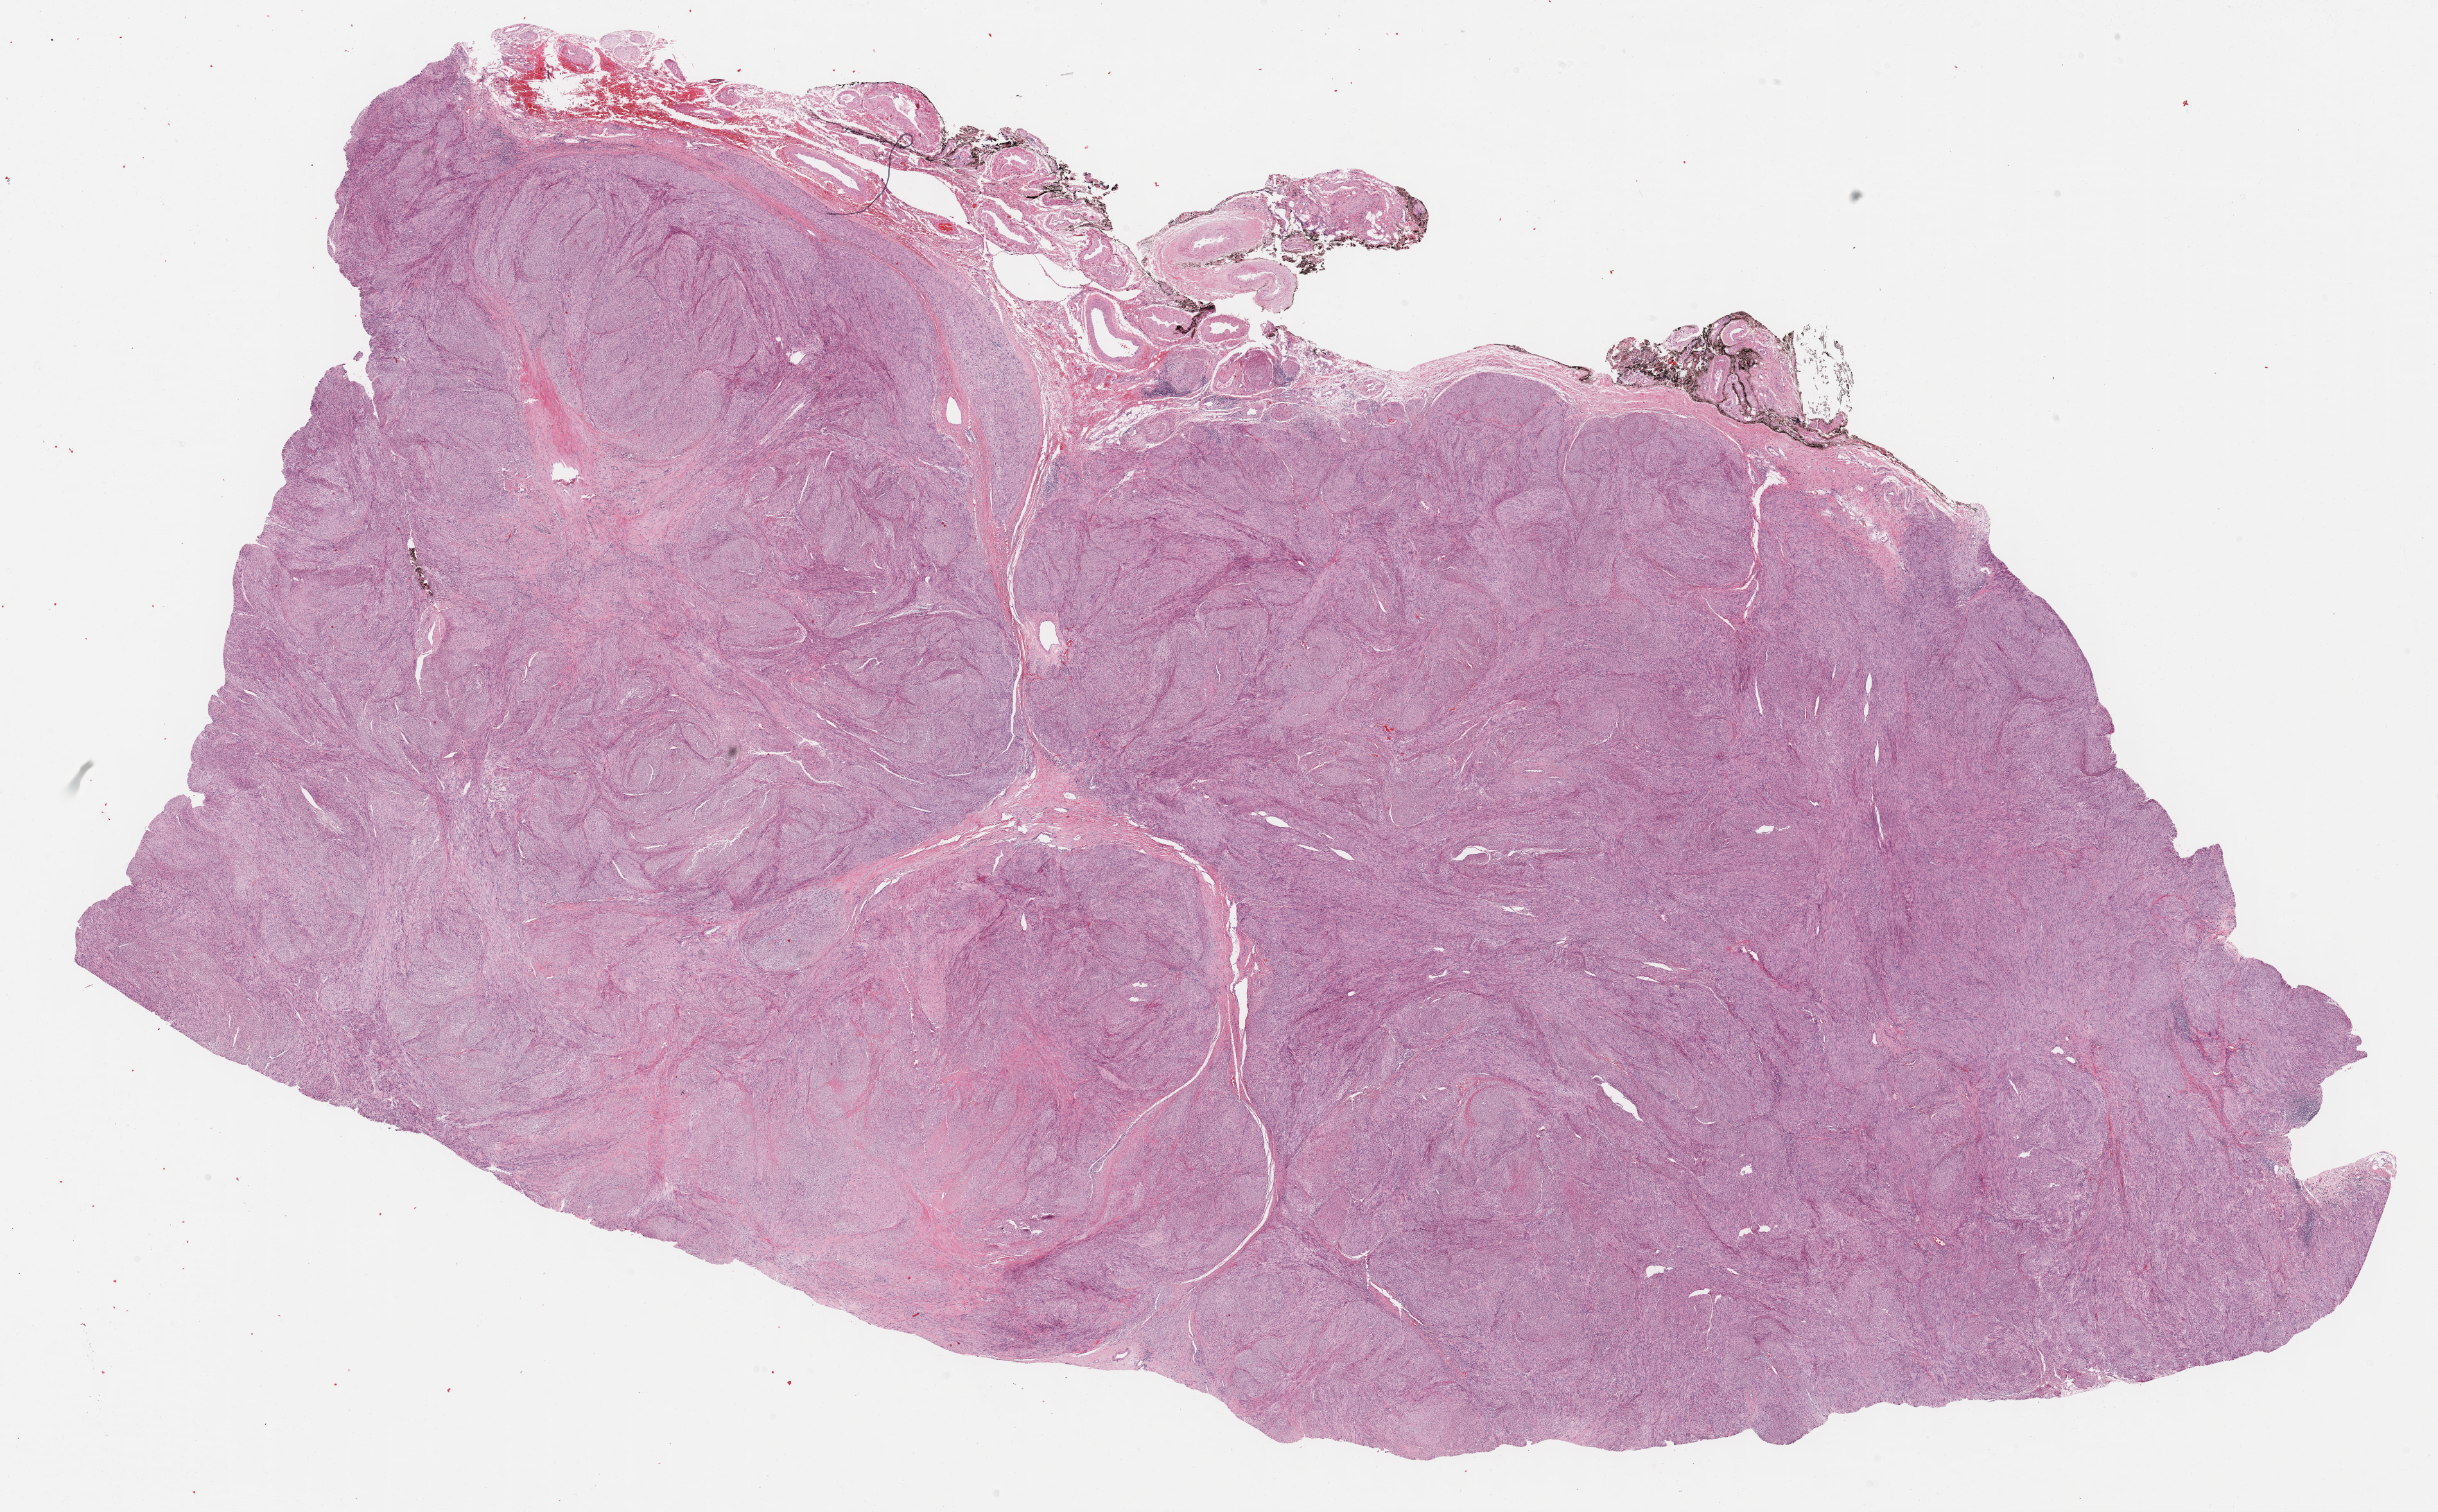
Whole-slide histology image, H&E — shown as a low-resolution overview of the whole scanned area (about 30.7 x 19.0 mm). Formalin-fixed paraffin-embedded (FFPE) diagnostic section. Sample: primary tumour, retroperitoneum and peritoneum. Female, age 78 years at initial diagnosis.
Histologic diagnosis: Dedifferentiated liposarcoma.